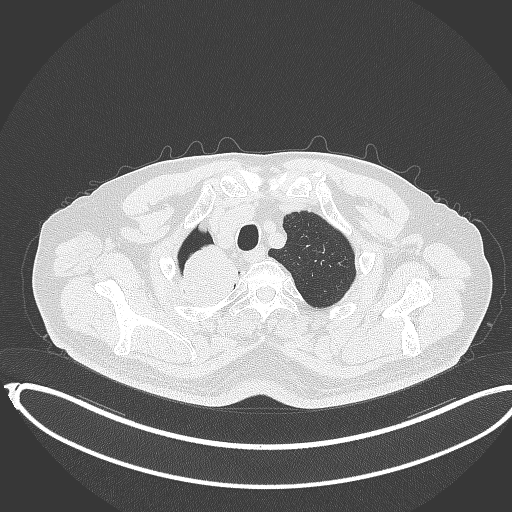
Chest CT, one axial slice; position 327 of 403 along the scan axis; reconstruction kernel B70f; 120 kVp; lung window (W 1500 / L -600 HU); 1 mm slice thickness; 512 × 512 image matrix, field of view 436 × 436 mm. Male patient, age 68 years. From the clinical record (not read from this slice): clinical TNM (as recorded): T2a N0 M0.
Annotated regions visible in this slice (bounding box drawn by a radiologist):
- lung tumour (recorded histology: adenocarcinoma): bounding box <176,239,249,314> (left, top, right, bottom; pixels)